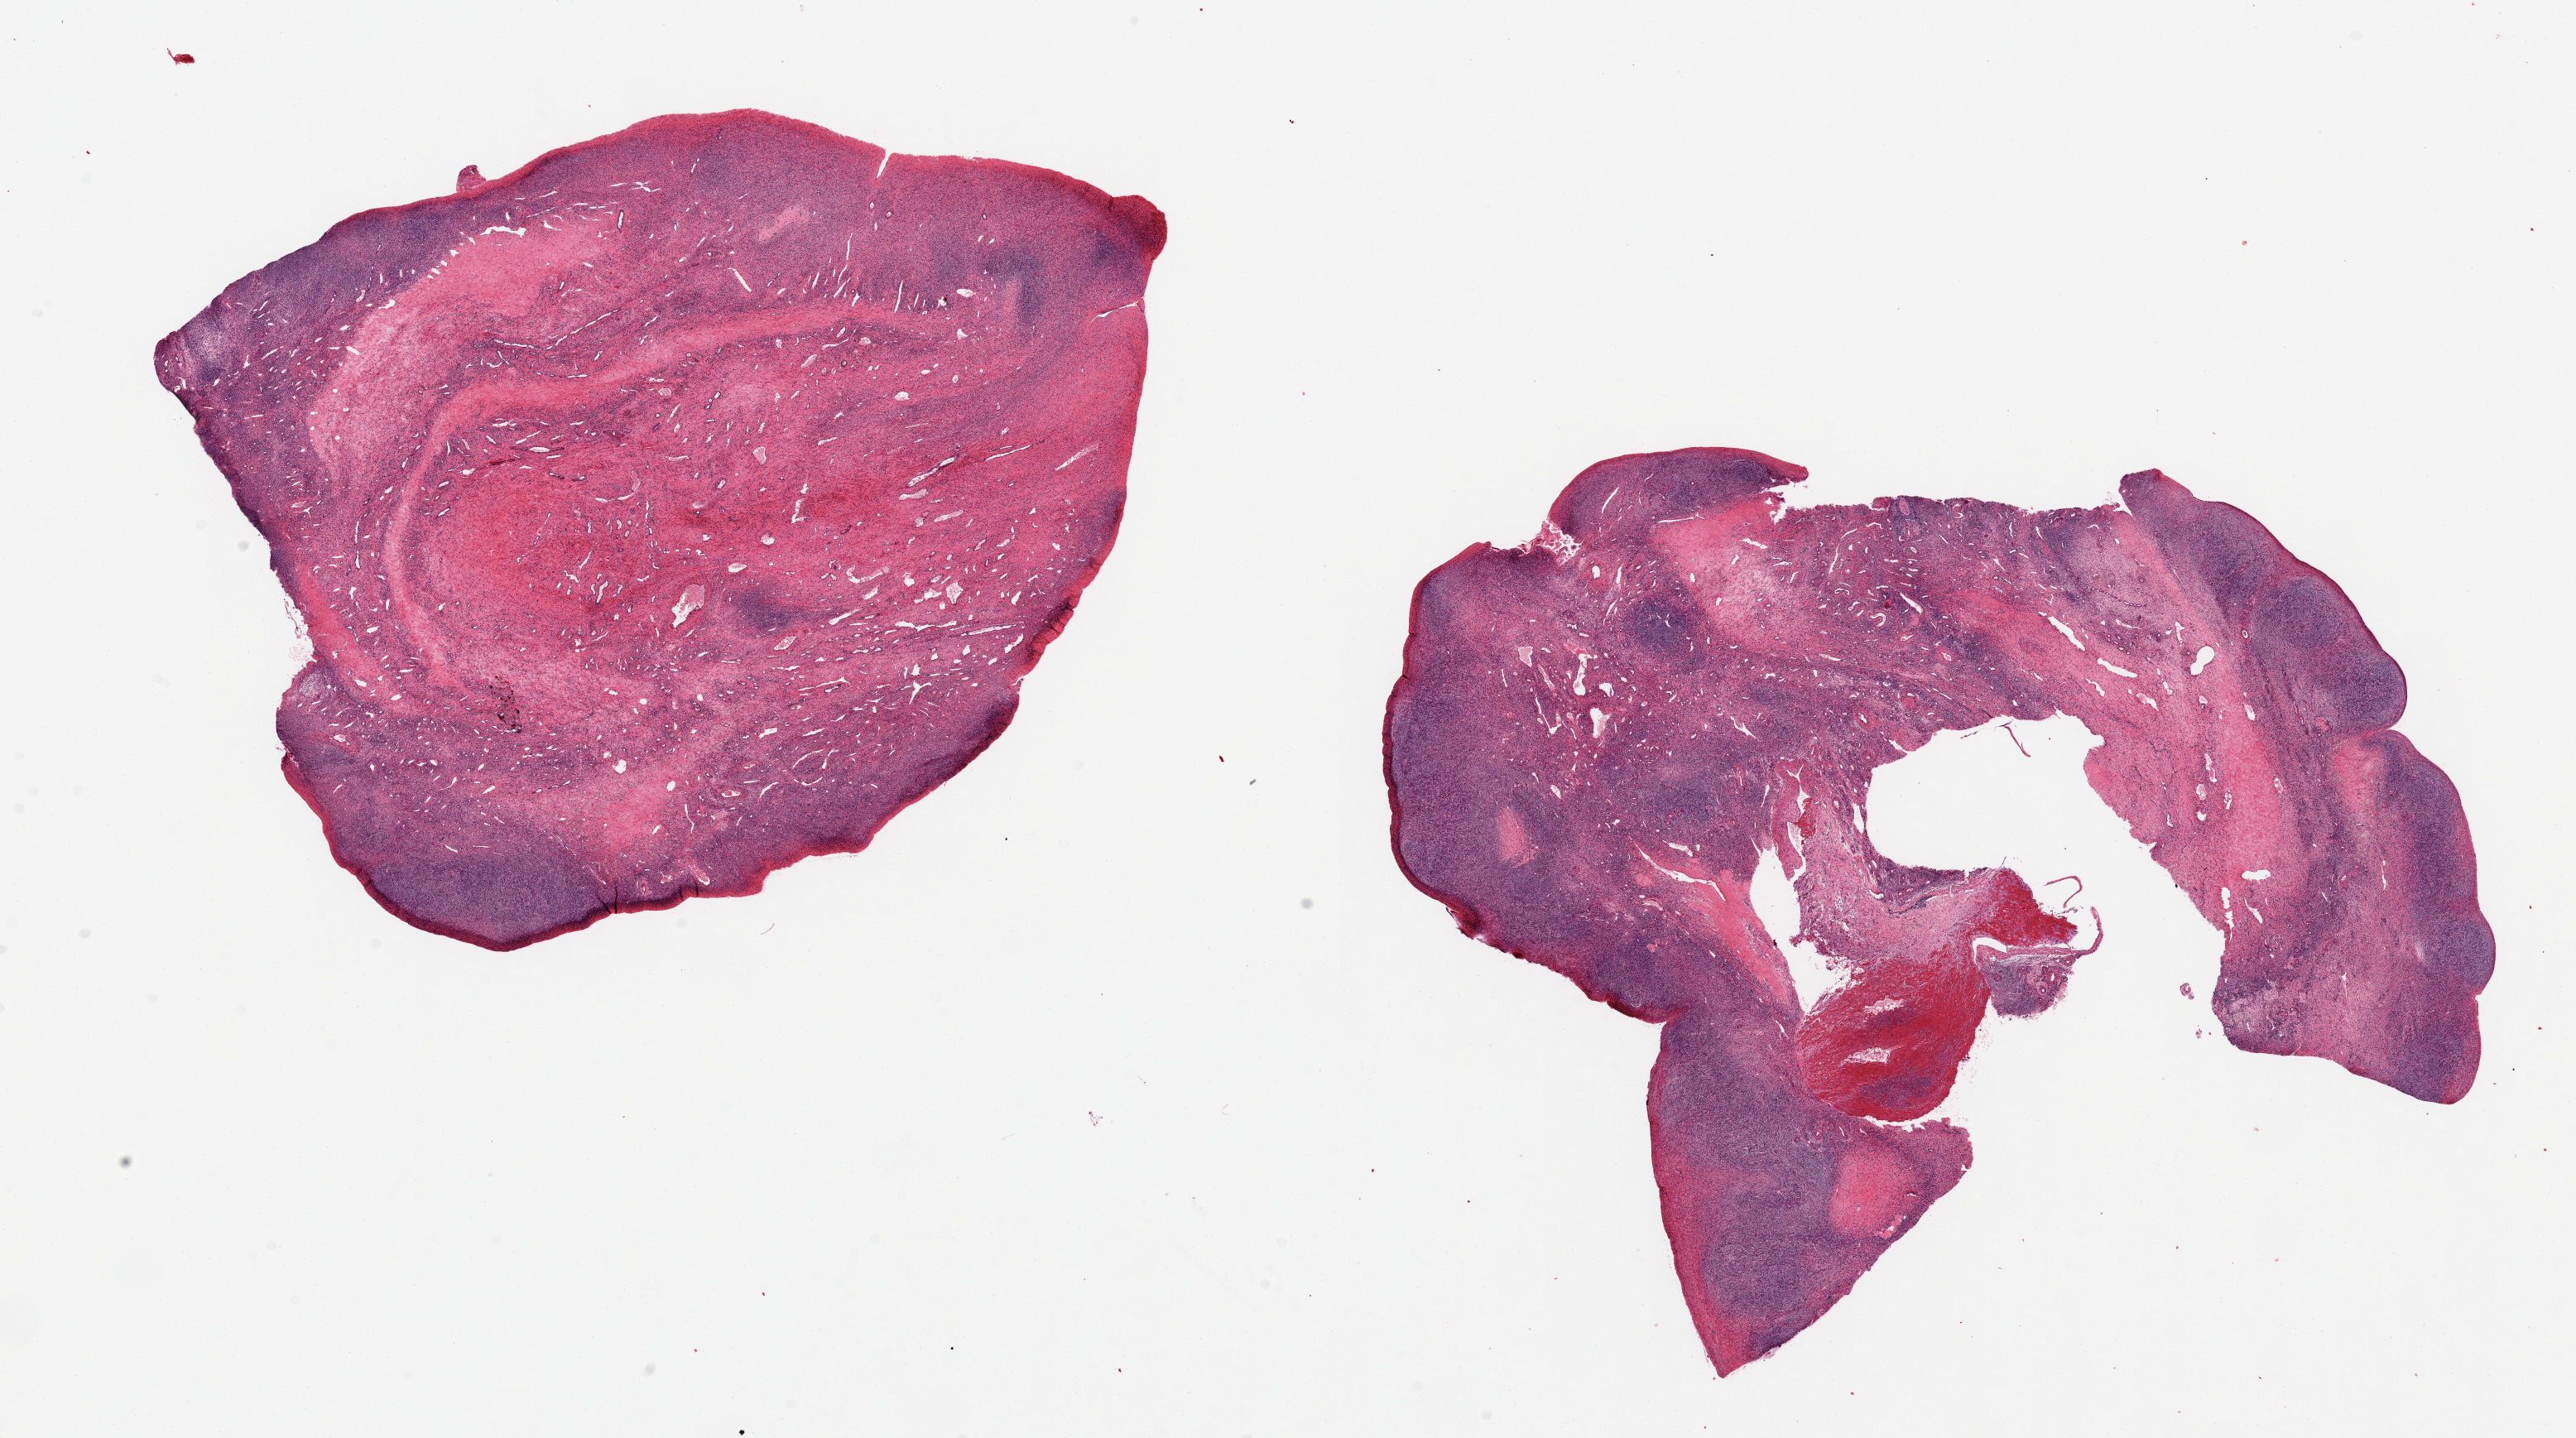
Whole-slide image, hematoxylin and eosin (H&E) stain, brightfield, low-resolution overview of the scanned area, about 24.6 x 13.7 mm (acquisition: 20x scan), PAXgene-fixed paraffin-embedded (PFPE) section, sampled site (target tissue): ovary, donor tissue sample. Female donor.
• reviewer comment on this tissue sample: 2 aliquots, ~ 9x7mm. Rare residual oocytes, involuting corpus luteum